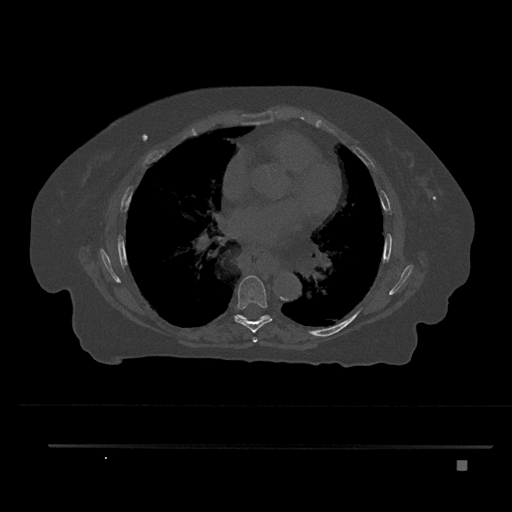
CT including the spine, one axial slice; position 481 of 797 along the scan axis; bone window (W 1800 / L 400 HU); 0.5 mm slice thickness; 512 × 512 image matrix. Patient: female, 76 years. From the clinical record (not read from this slice): primary cancer: lung; vertebrae with lytic lesions (as recorded): T11, L3.
Structures marked on this image (semi-automatically segmented with operator editing):
- T6 vertebra: bounding box <252,337,258,343> (left, top, right, bottom; pixels)
- T7 vertebra: <234,275,272,333>
- T8 vertebra: <236,315,270,321>